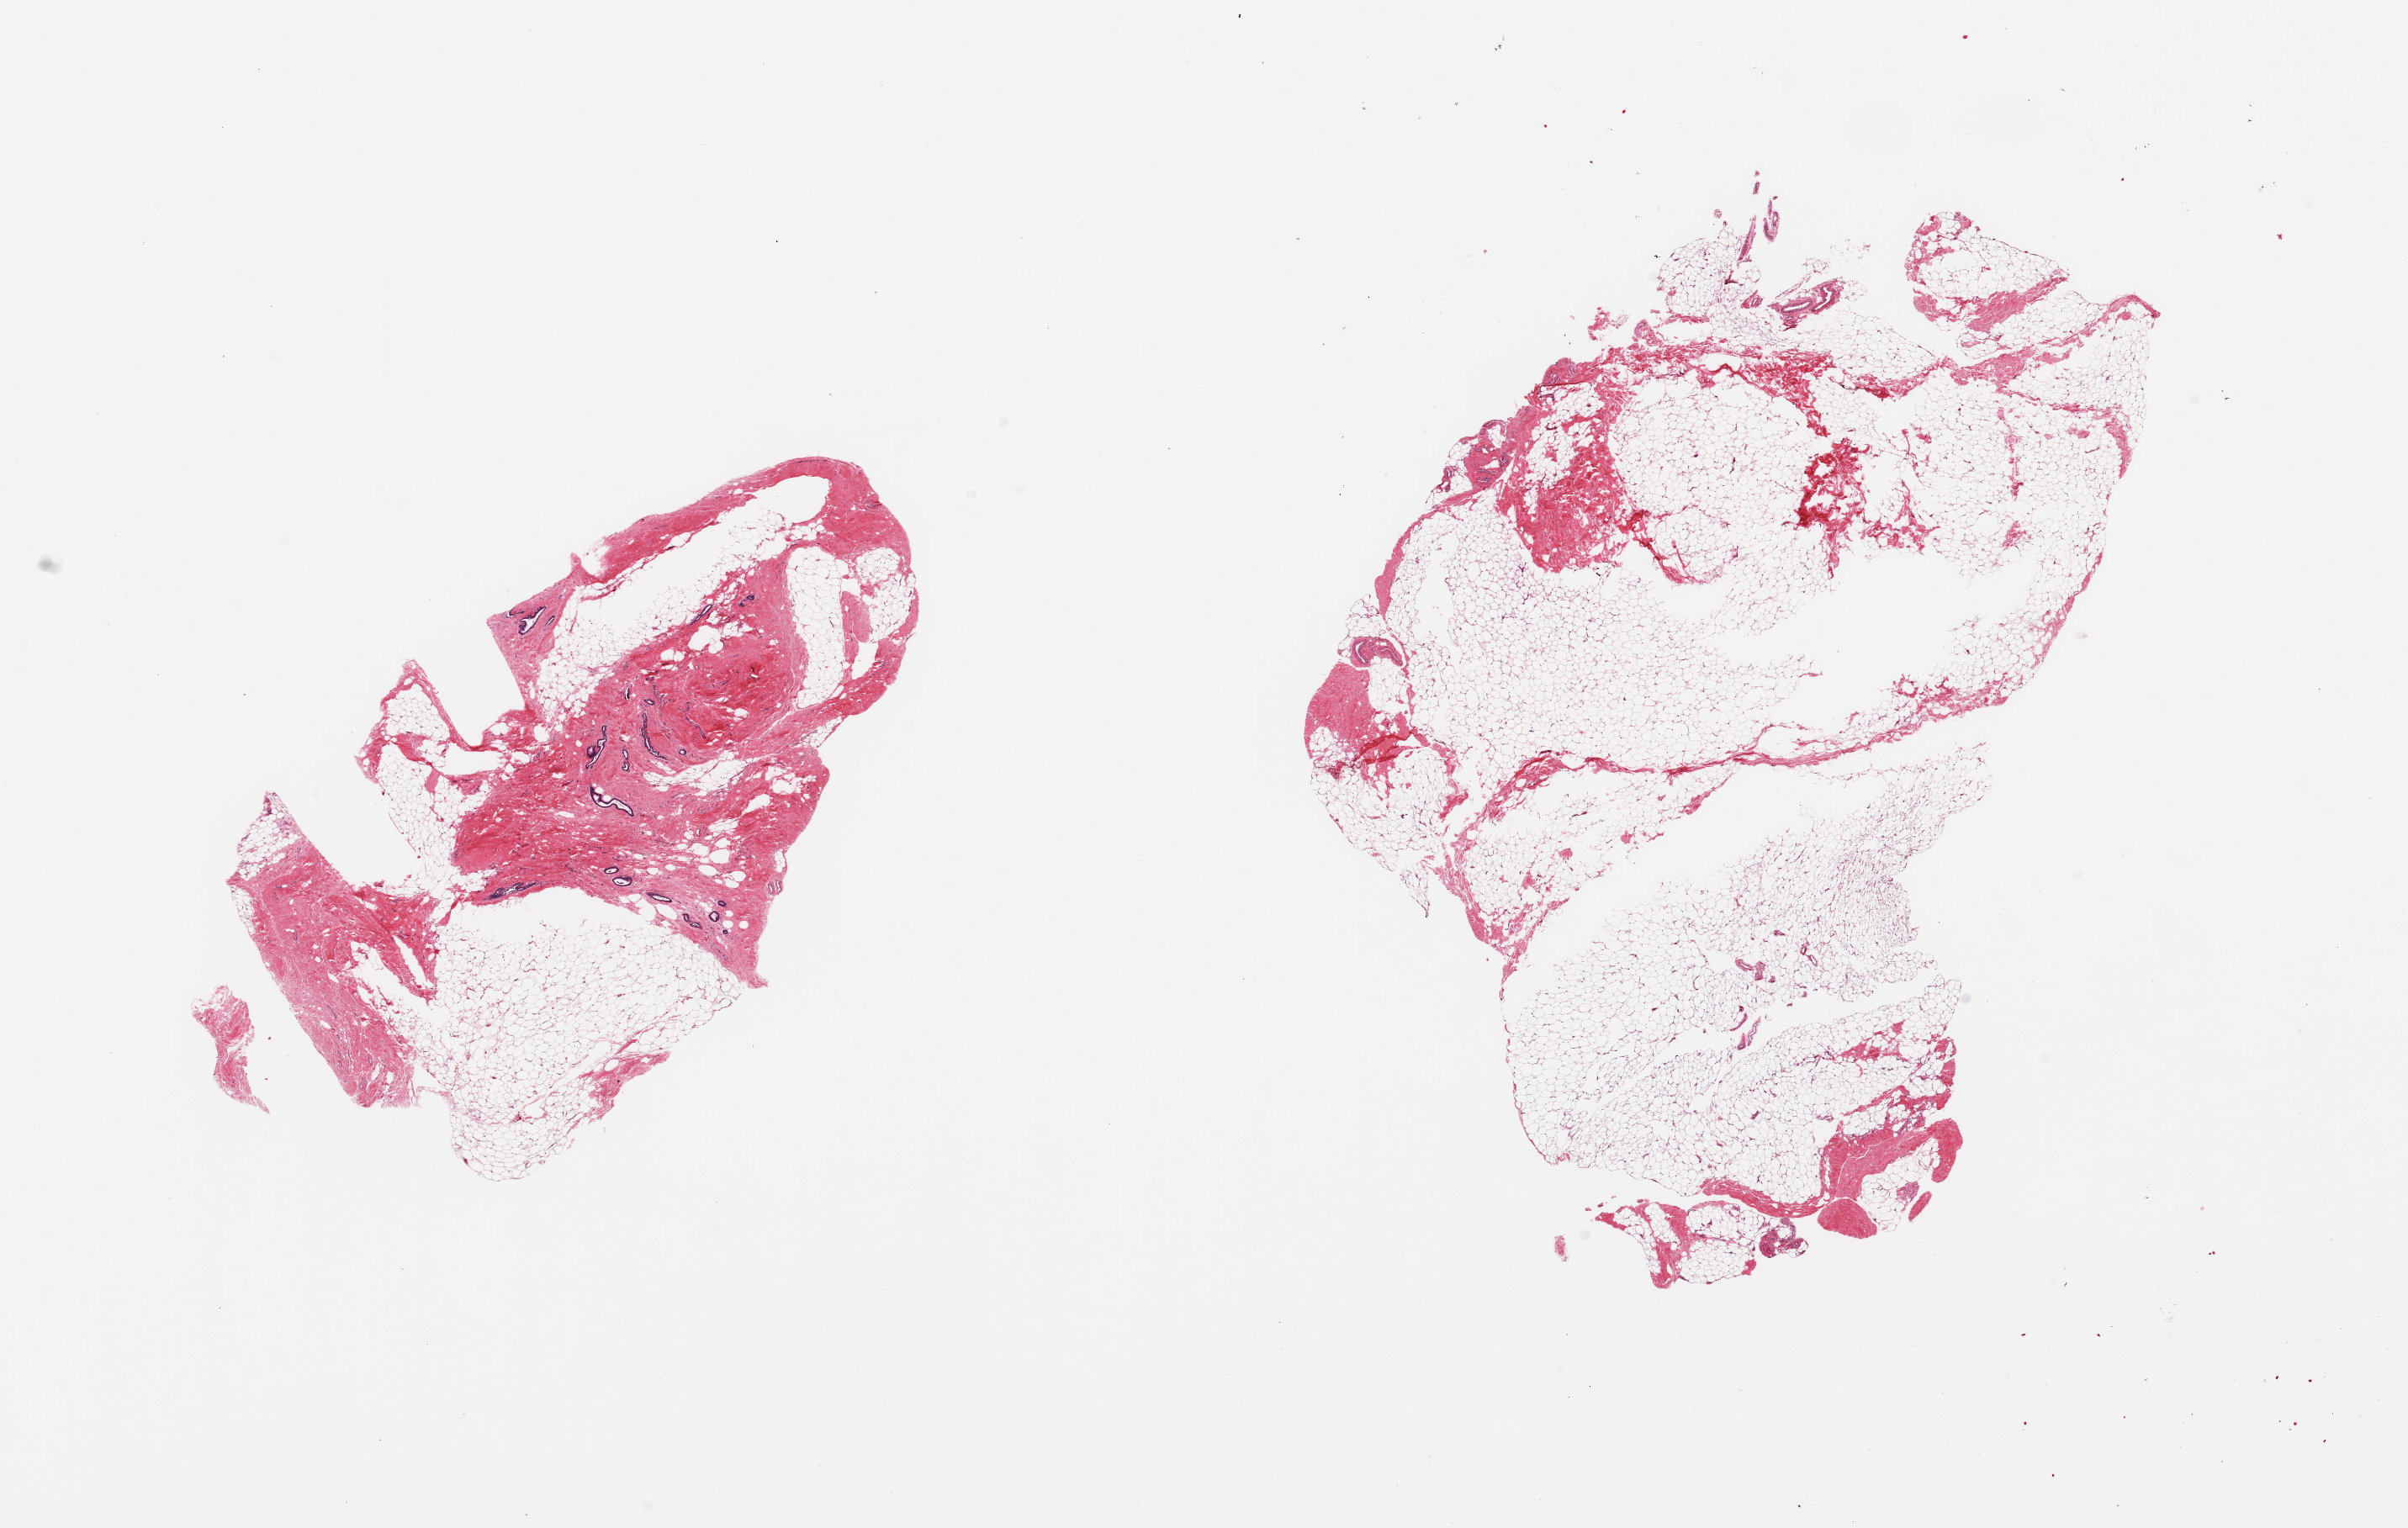
Digitized hematoxylin and eosin (H&E)-stained section, shown as a low-resolution overview of the whole scanned area (about 22.6 x 14.4 mm), PAXgene-fixed paraffin-embedded (PFPE) section, section of breast (target tissue), donor tissue sample. Donor: male.
• pathologist's review note for this sample: 2 pieces; smaller piece has ductal and fibrous tissue with gynecomastoid changes; other piece is fibroadipose without ductal elements